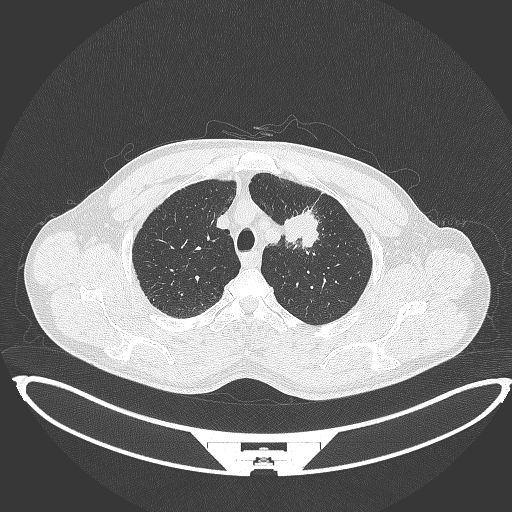
Chest CT, one axial slice; slice 360 of 395 in the series (ordered by position); reconstruction kernel B70f; lung window (W 1500 / L -600 HU); 512 × 512 image matrix. Patient: male, 60 years. From the clinical record (not read from this slice): clinical TNM (as recorded): T2a N0 M0; histopathological grade: G1-G2.
Outlined on this slice (bounding box drawn by a radiologist):
- lung tumour (recorded histology: squamous cell carcinoma): bounding box (x1, y1, x2, y2) in pixels: (281, 209, 323, 252)